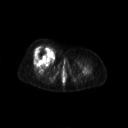
FDG PET of an extremity soft-tissue mass (from a PET/CT study), one axial slice; position 52 of 267 along the scan axis; 3.27 mm slice thickness; 128 × 128 image matrix, field of view 700 × 700 mm. Female patient, age 56 years. From the clinical record (not read from this slice): histological type: malignant solitary fibrous tumor; grade: intermediate; site of the primary tumour: right thigh.
Annotated regions visible in this slice (expert contour drawn on MRI and transferred to this co-registered scan by the dataset authors):
- gross tumour volume including surrounding oedema: bounding box <32,46,55,62> (left, top, right, bottom; pixels)
- gross tumour volume (mass): <32,46,54,62>